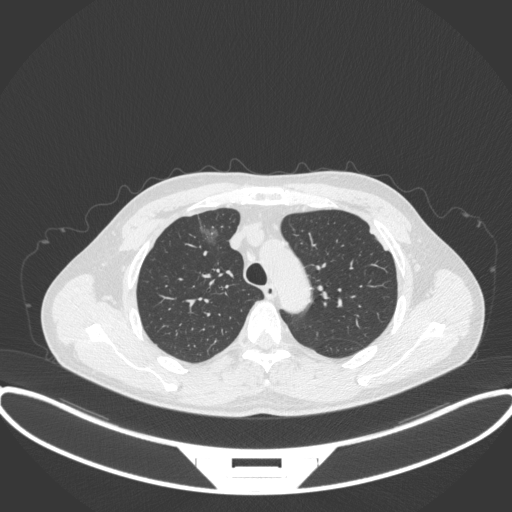
Chest CT, one axial slice; position 275 of 395 along the scan axis; reconstruction kernel B31f; 120 kVp; lung window (W 1500 / L -600 HU); 1 mm slice thickness; 512 × 512 image matrix, field of view 424 × 424 mm. Patient: male, 60 years. Case-level facts recorded for this patient, not image findings: clinical TNM (as recorded): T1c N0 M0.
Structures marked on this image (bounding box drawn by a radiologist):
- lung tumour (recorded histology: adenocarcinoma): bounding box [x1, y1, x2, y2] px = [192, 212, 231, 253]